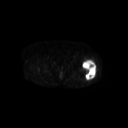
FDG PET of an extremity soft-tissue mass (from a PET/CT study), one axial slice. Position 246 of 267 along the scan axis. 3.27 mm slice thickness. 128 × 128 image matrix. Patient: female, 62 years. Case-level facts recorded for this patient, not image findings: histological type: undifferentiated – high grade; grade: high; site of the primary tumour: left thigh.
Structures marked on this image (expert contour drawn on MRI and transferred to this co-registered scan by the dataset authors):
- gross tumour volume including surrounding oedema: bounding box <81,60,96,81> (left, top, right, bottom; pixels)
- gross tumour volume (mass): <82,61,96,80>